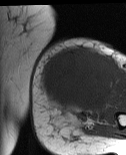
MRI of an extremity soft-tissue mass, one axial slice; slice 24 of 86 in the series (ordered by position); MR volume resampled by the dataset authors to the PET/CT grid (not the native acquisition matrix); 3.27 mm slice thickness; 126 × 155 image matrix, field of view 123 × 151 mm. Female patient. Case-level facts recorded for this patient, not image findings: histological type: pleiomorphic leiomyosarcoma; grade: high; site of the primary tumour: left biceps.
Outlined on this slice (expert contour drawn on MRI and transferred to this co-registered scan by the dataset authors):
- gross tumour volume including surrounding oedema: bounding box <40,47,117,114> (left, top, right, bottom; pixels)
- gross tumour volume (mass): <40,47,117,110>